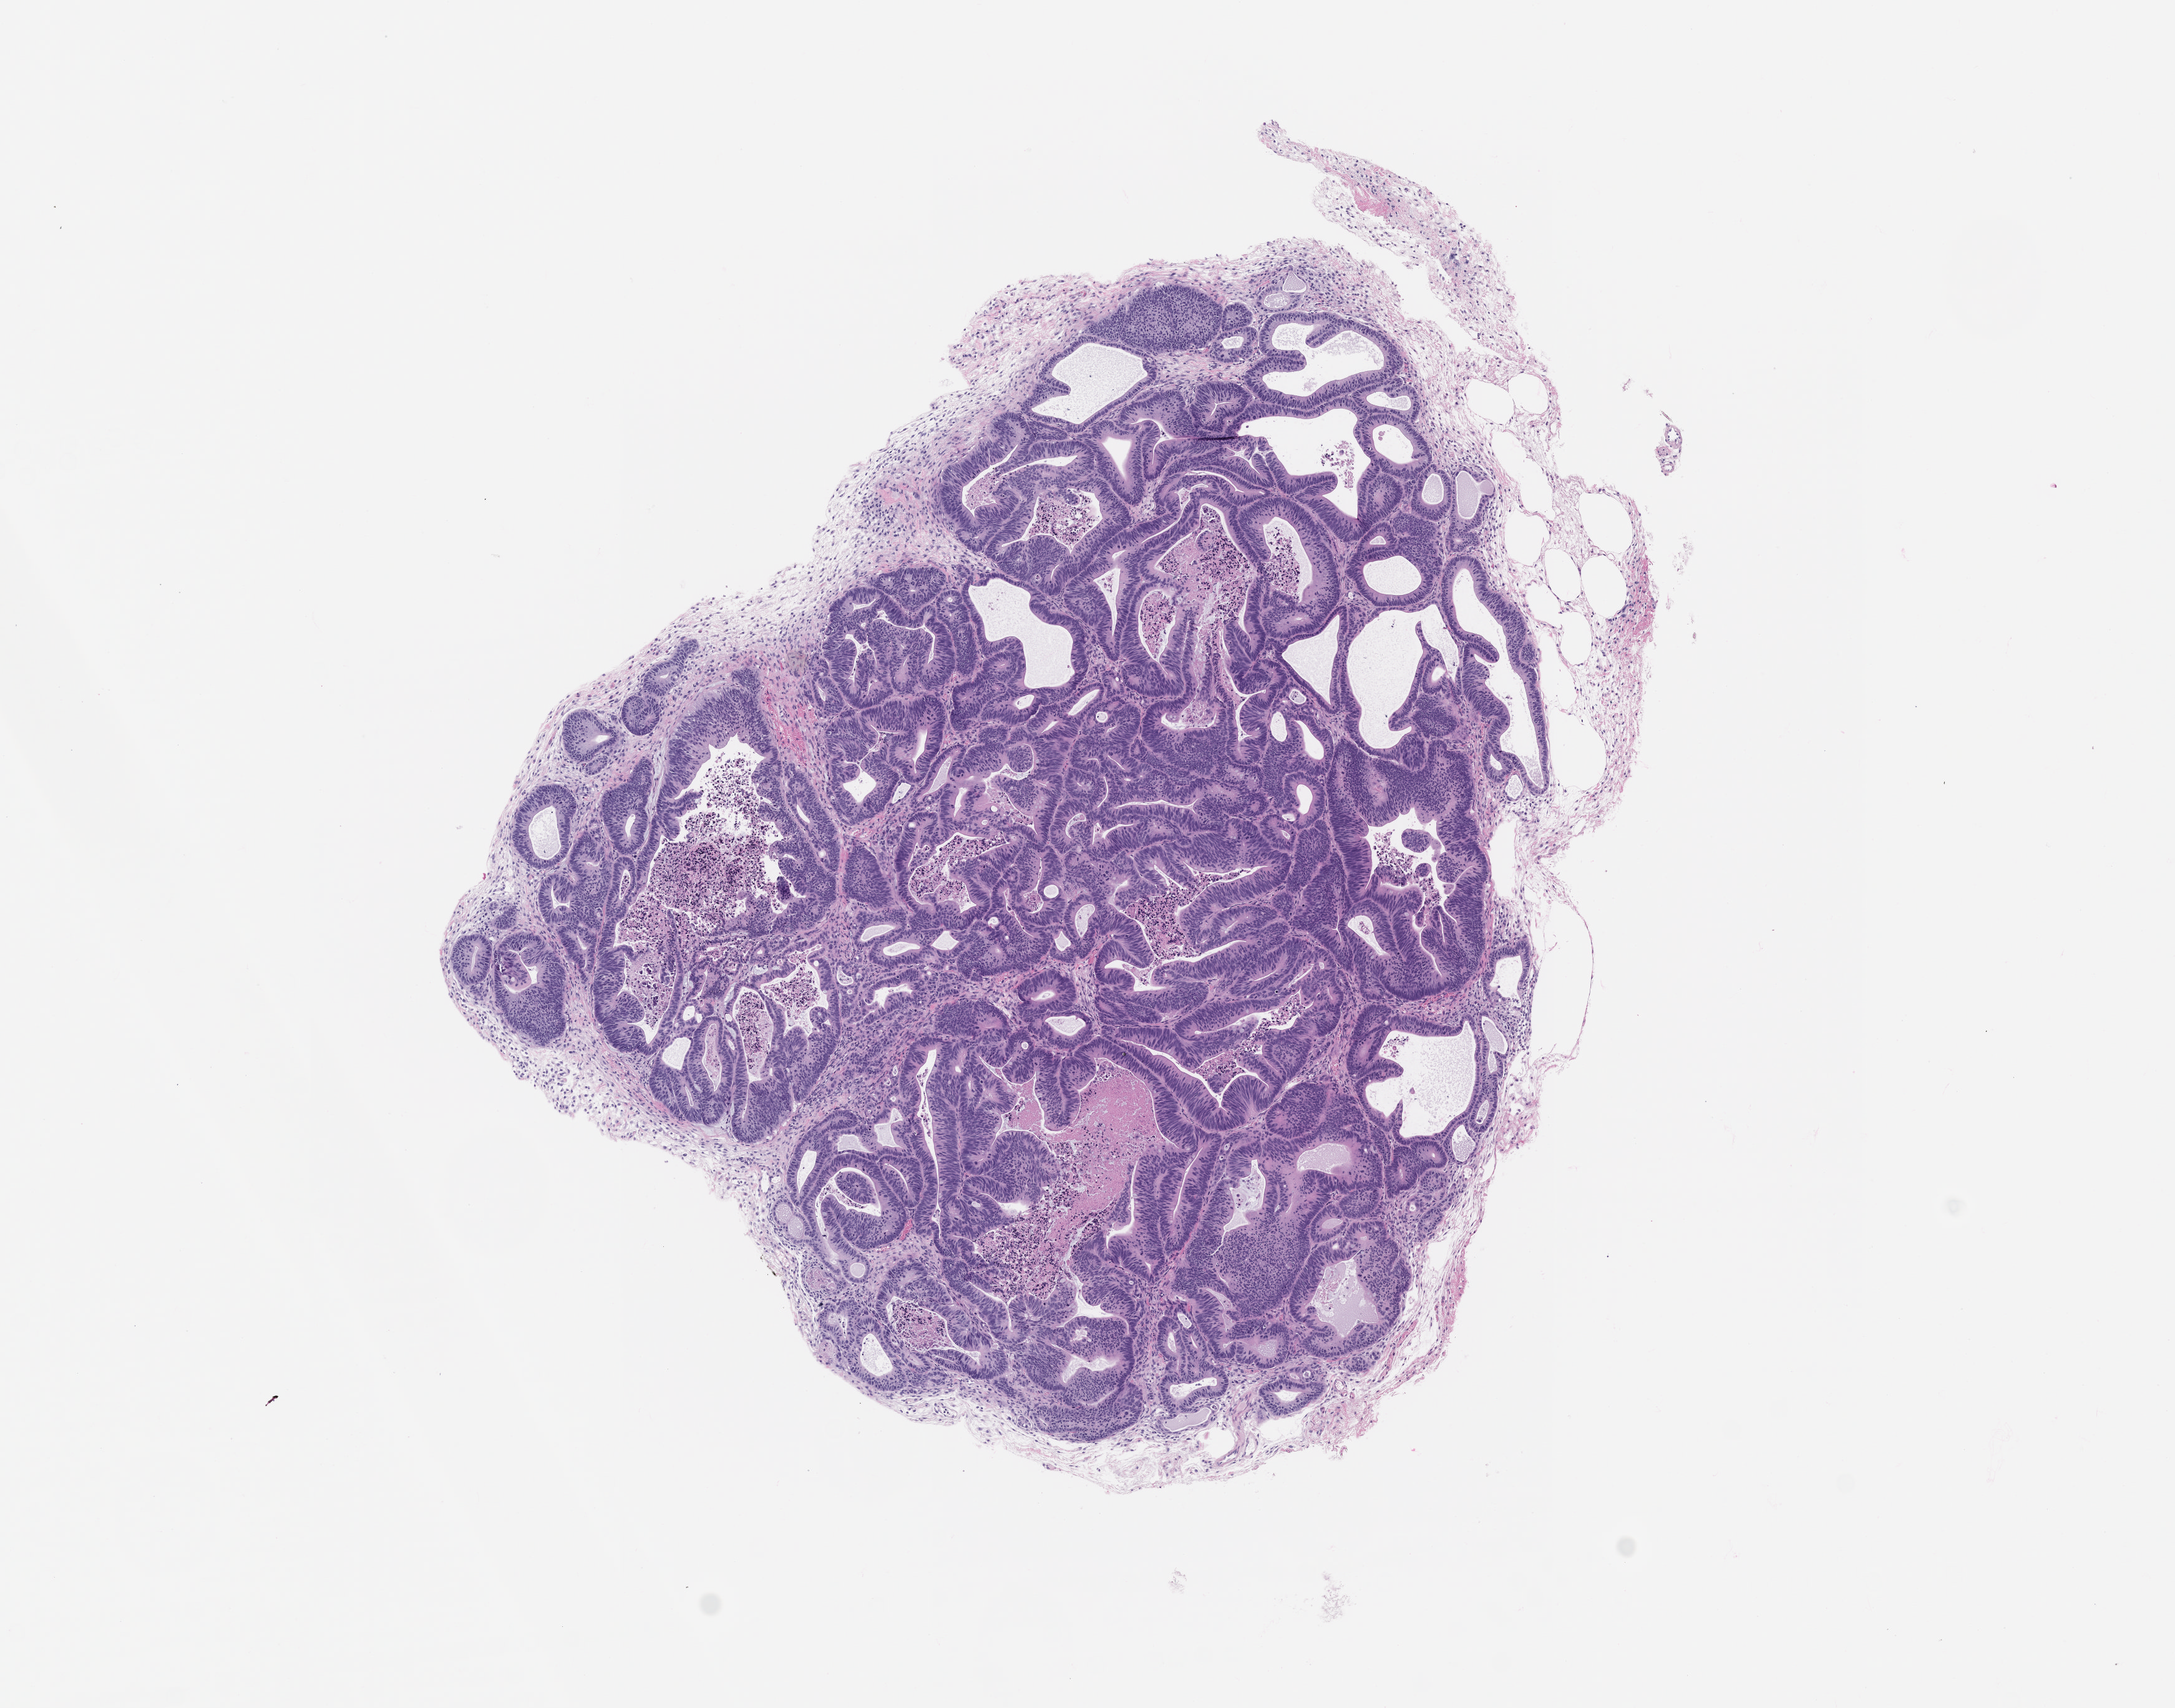
Whole-slide image, haematoxylin and eosin: patient-derived xenograft (human tumor grown in a mouse), passage 0, a low-resolution overview of the entire scanned area, about 7.0 x 5.5 mm, formalin-fixed paraffin-embedded section, originating tumor site category: colon.
• originating patient diagnosis: Colon Adenocarcinoma